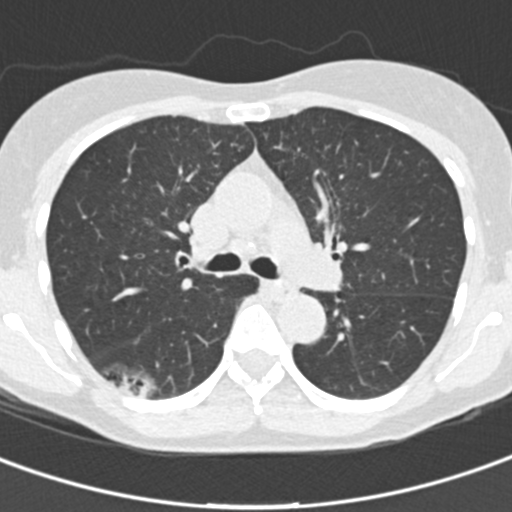
Chest CT (low-dose screening protocol), one axial image; baseline screening round; lung window (W 1500 / L -600 HU); slice 64 of 162 in the series; 512 × 512 image matrix. Female, age 64 years at enrolment.
Lesion marked by an expert reader, bounding box [x1, y1, x2, y2] px = [84, 348, 176, 416]. Reader record for this screening exam (exam-level; its link to the box is not recorded): non-calcified nodule or mass ≥4 mm, right lower lobe, 31 × 15 mm, poorly defined margins, ground glass attenuation. Participant outcome: lung cancer diagnosed 91 days after this screen — bronchiolo-alveolar carcinoma, non-mucinous, right lower lobe, well differentiated (G1), stage IA (AJCC 6th edition), 20 mm at pathology.